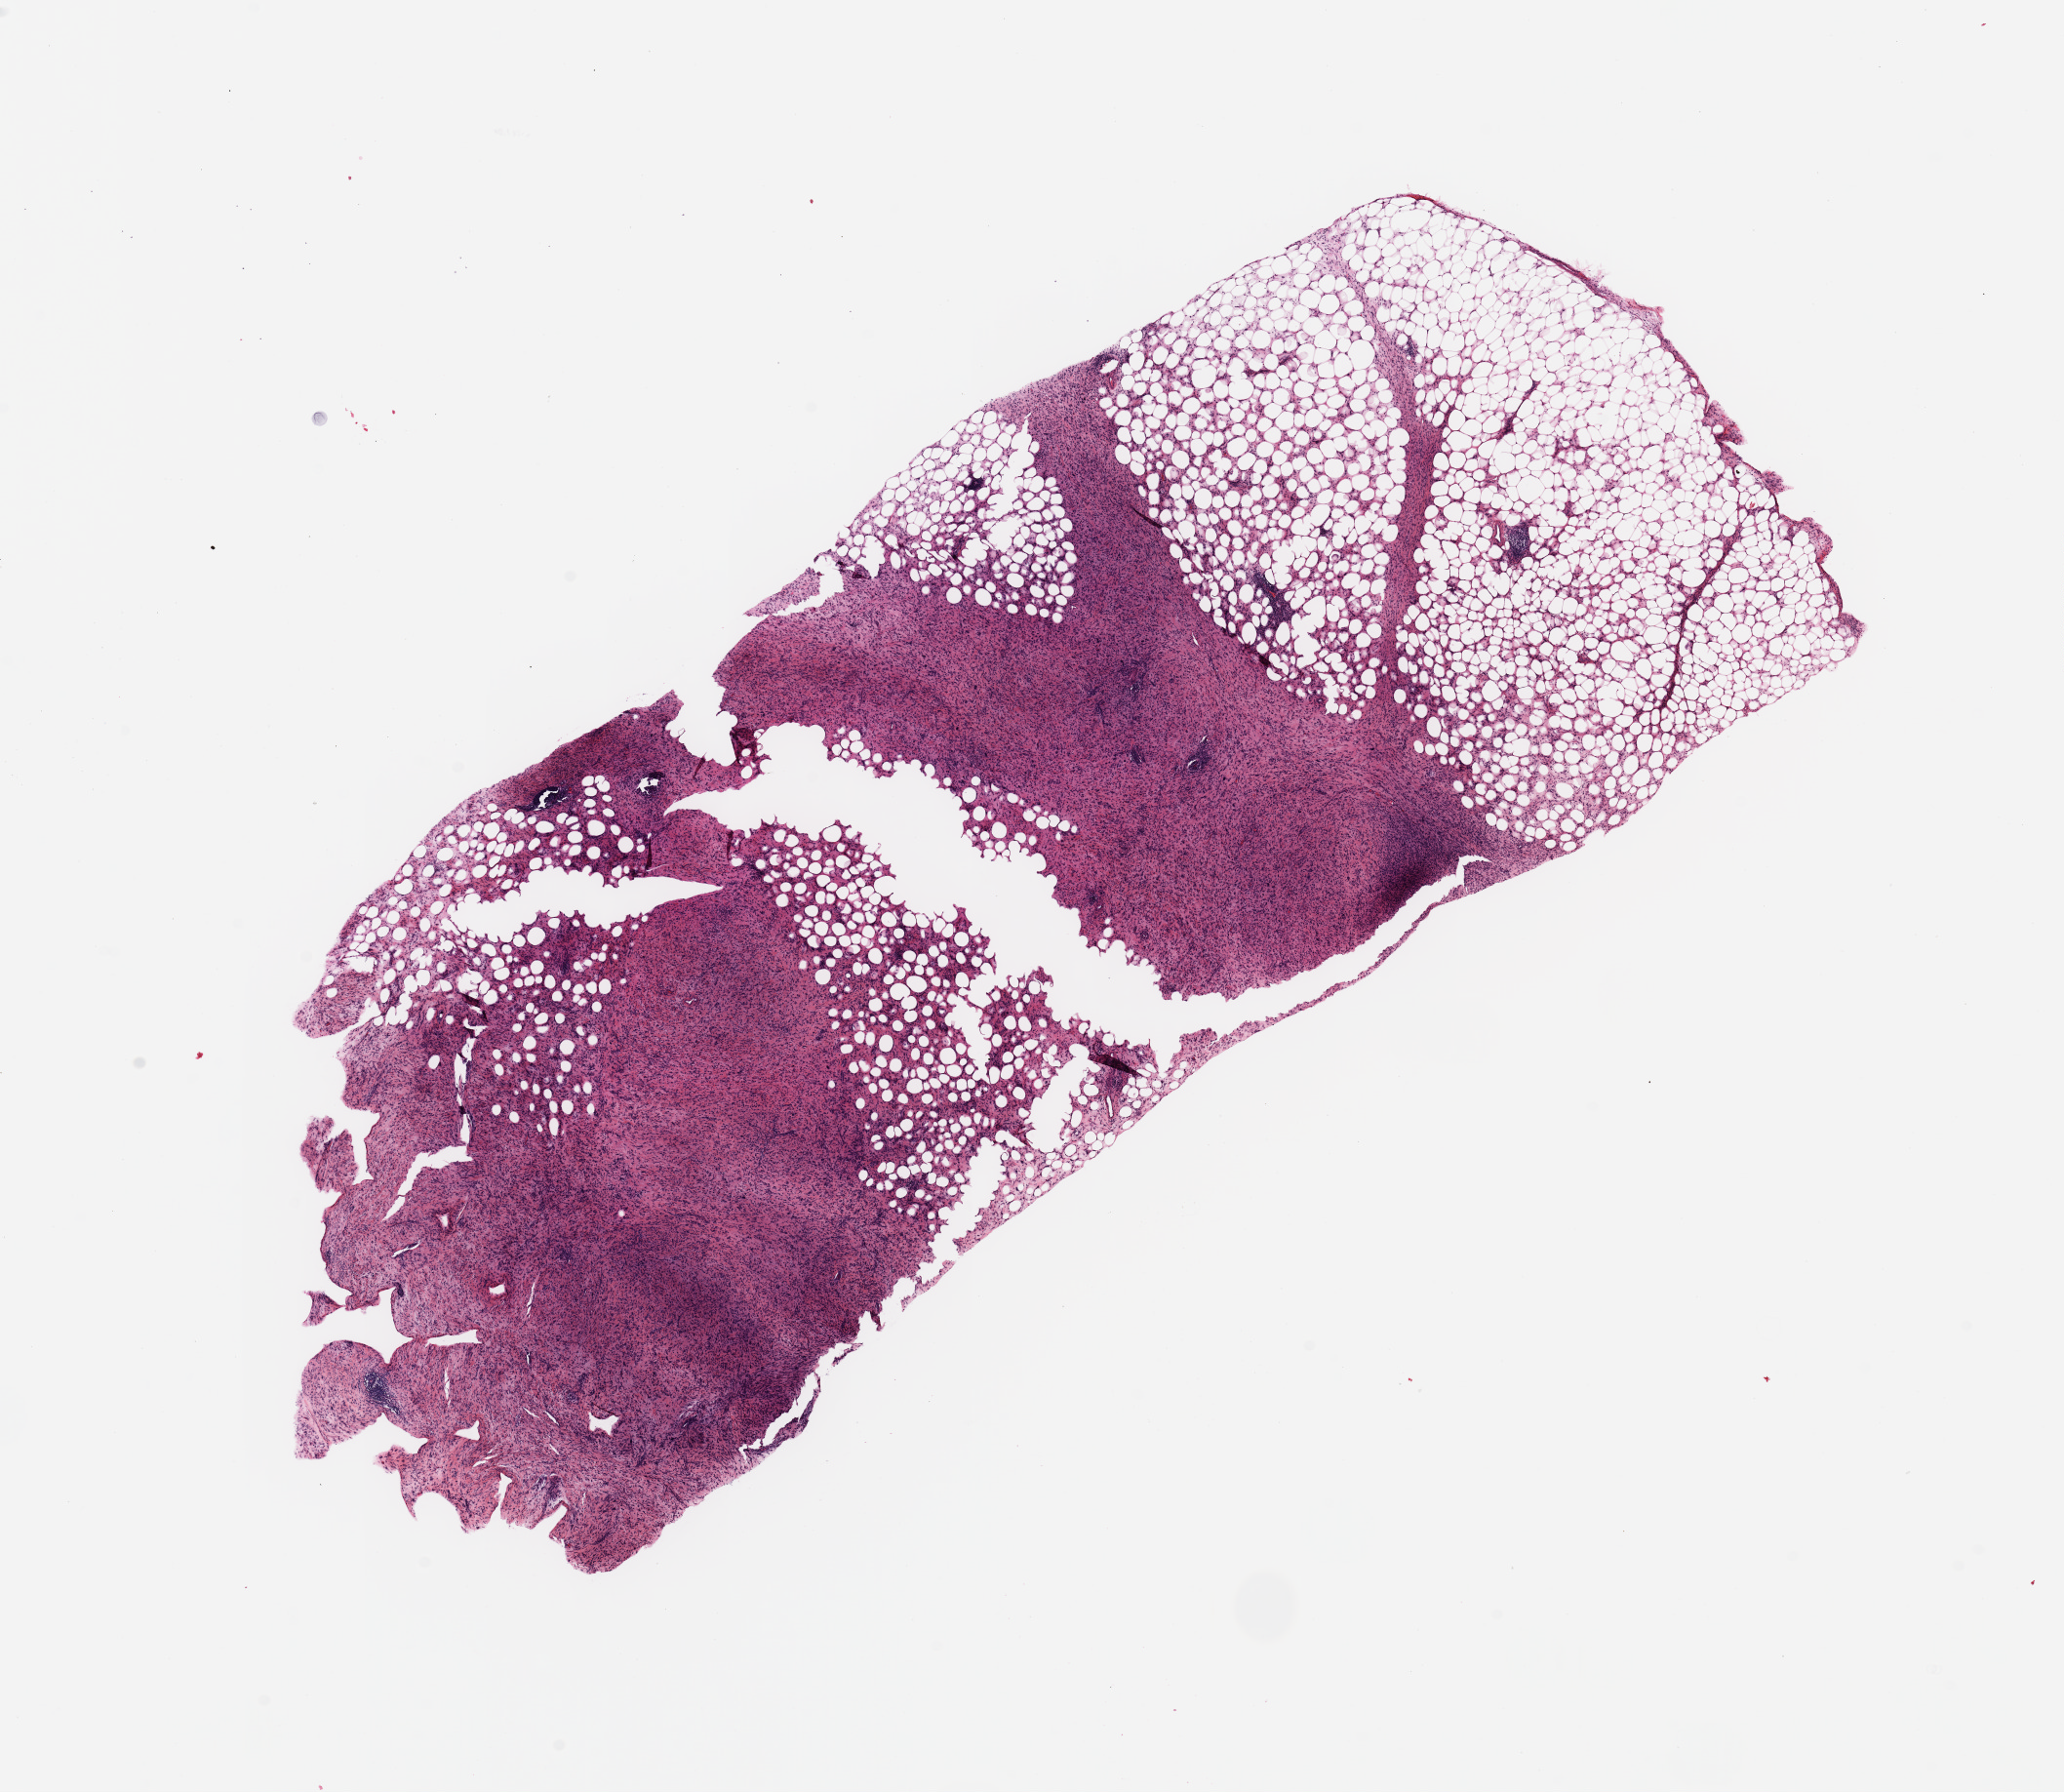
H&E-stained whole-slide image, whole scanned area (about 16.7 x 14.5 mm) shown as a low-resolution overview. Tumour tissue sample. 52-year-old male patient.
Primary tumour site (as recorded): retroperitoneum. Patient diagnosis (cohort enrolment): sarcoma (site not recorded at cohort level).